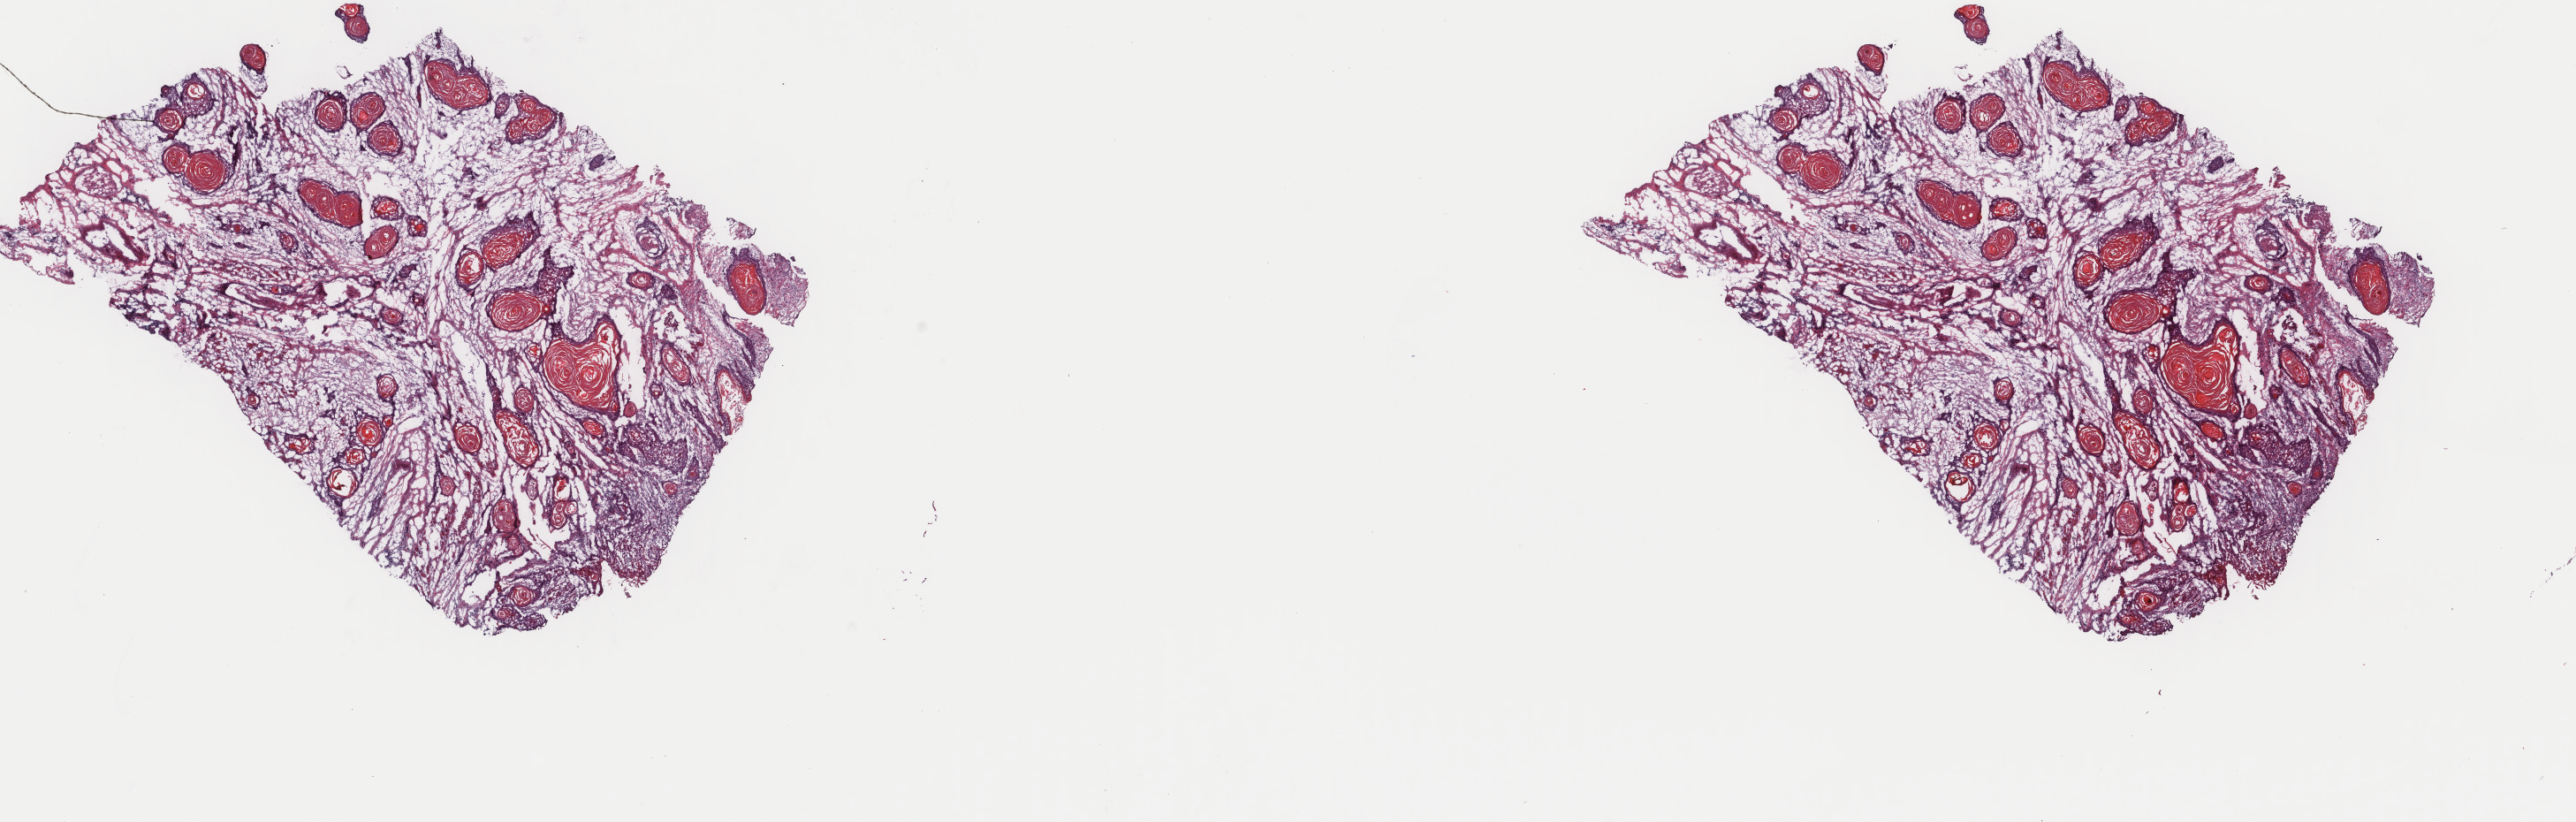
Digitized H&E tissue section (whole slide) — shown as a low-resolution overview of the whole scanned area (about 23.1 x 7.4 mm, acquisition: 40x scan), frozen section, head and neck, primary tumour sample. Patient: male, age at initial diagnosis 48 years. Histologic grade: G2 (moderately differentiated). Pathologist review of this section (percent, as recorded): tumour cells 60%, tumour nuclei 65%, normal cells 40%, stromal cells 0%, necrosis 0%. Inflammatory infiltration, as recorded: lymphocyte infiltration 3%, monocyte infiltration 0%, neutrophil infiltration 0%.
Histologic diagnosis: Squamous cell carcinoma, NOS (cheek mucosa). Laterality: left. AJCC pathologic stage: III.